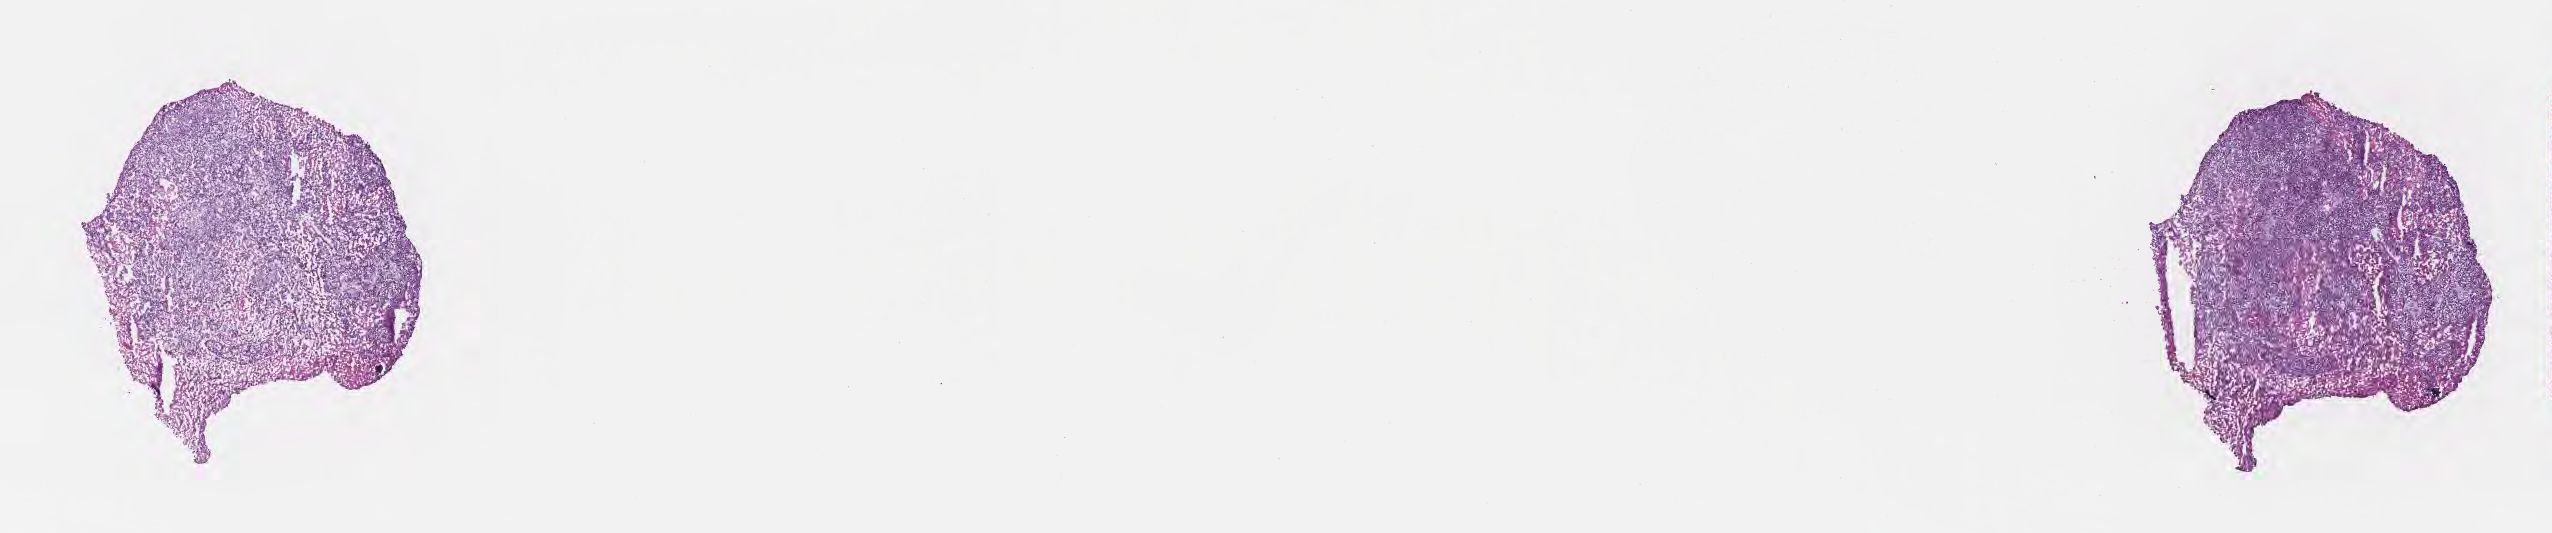
Whole-slide image, hematoxylin and eosin (H&E) stain, low-resolution overview of the scanned area, about 20.6 x 4.3 mm, cryosection, specimen: metastatic tumor tissue, resected from brain. Female patient; age at initial diagnosis 47 years. Pathologist review of this section (percent, as recorded): tumor cells 75%, tumor nuclei 75%, stromal cells 10%, necrosis 15%, normal cells 0%. Infiltration values recorded for this section: lymphocyte infiltration 4%, monocyte infiltration 1%, neutrophil infiltration 3%.
Section: bottom of the tissue portion. Patient diagnosis (primary): Malignant melanoma, NOS.